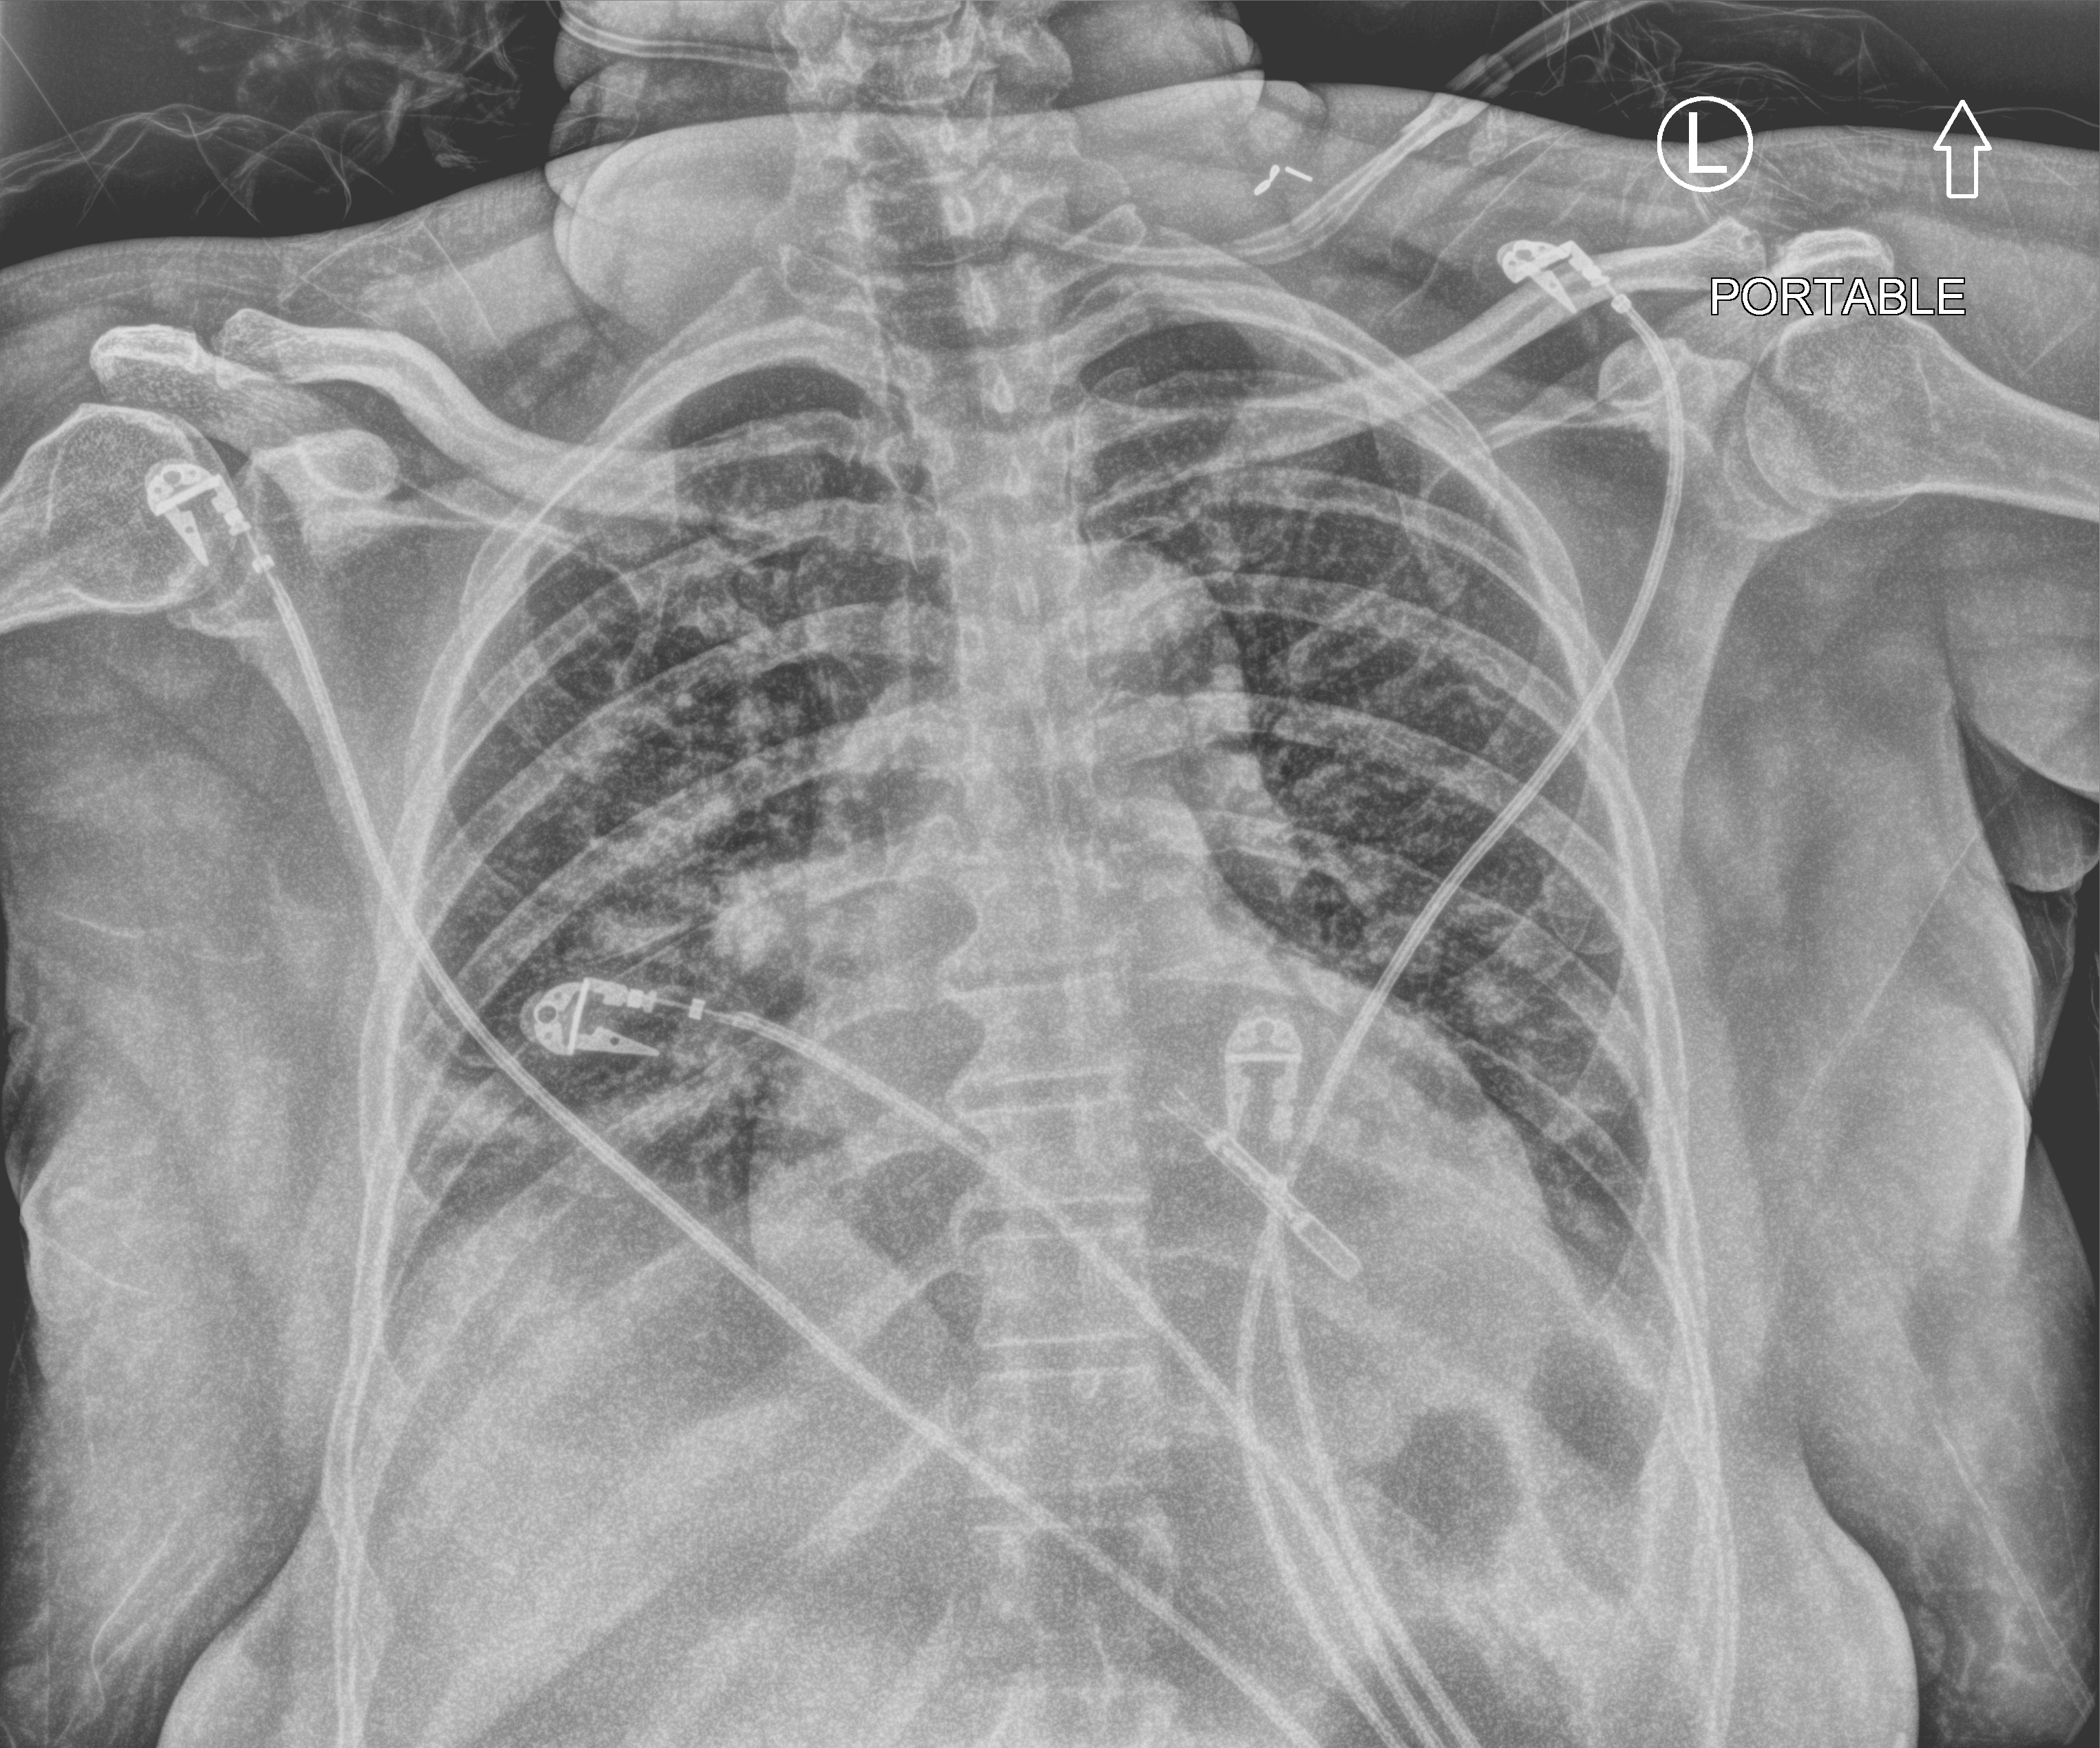
Portable chest radiograph. Patient hospitalised with COVID-19; female, aged 18–59 years.
Admission-level facts for this patient (not findings on this image; timing relative to this image not recorded):
- mechanically ventilated during this hospital stay: no